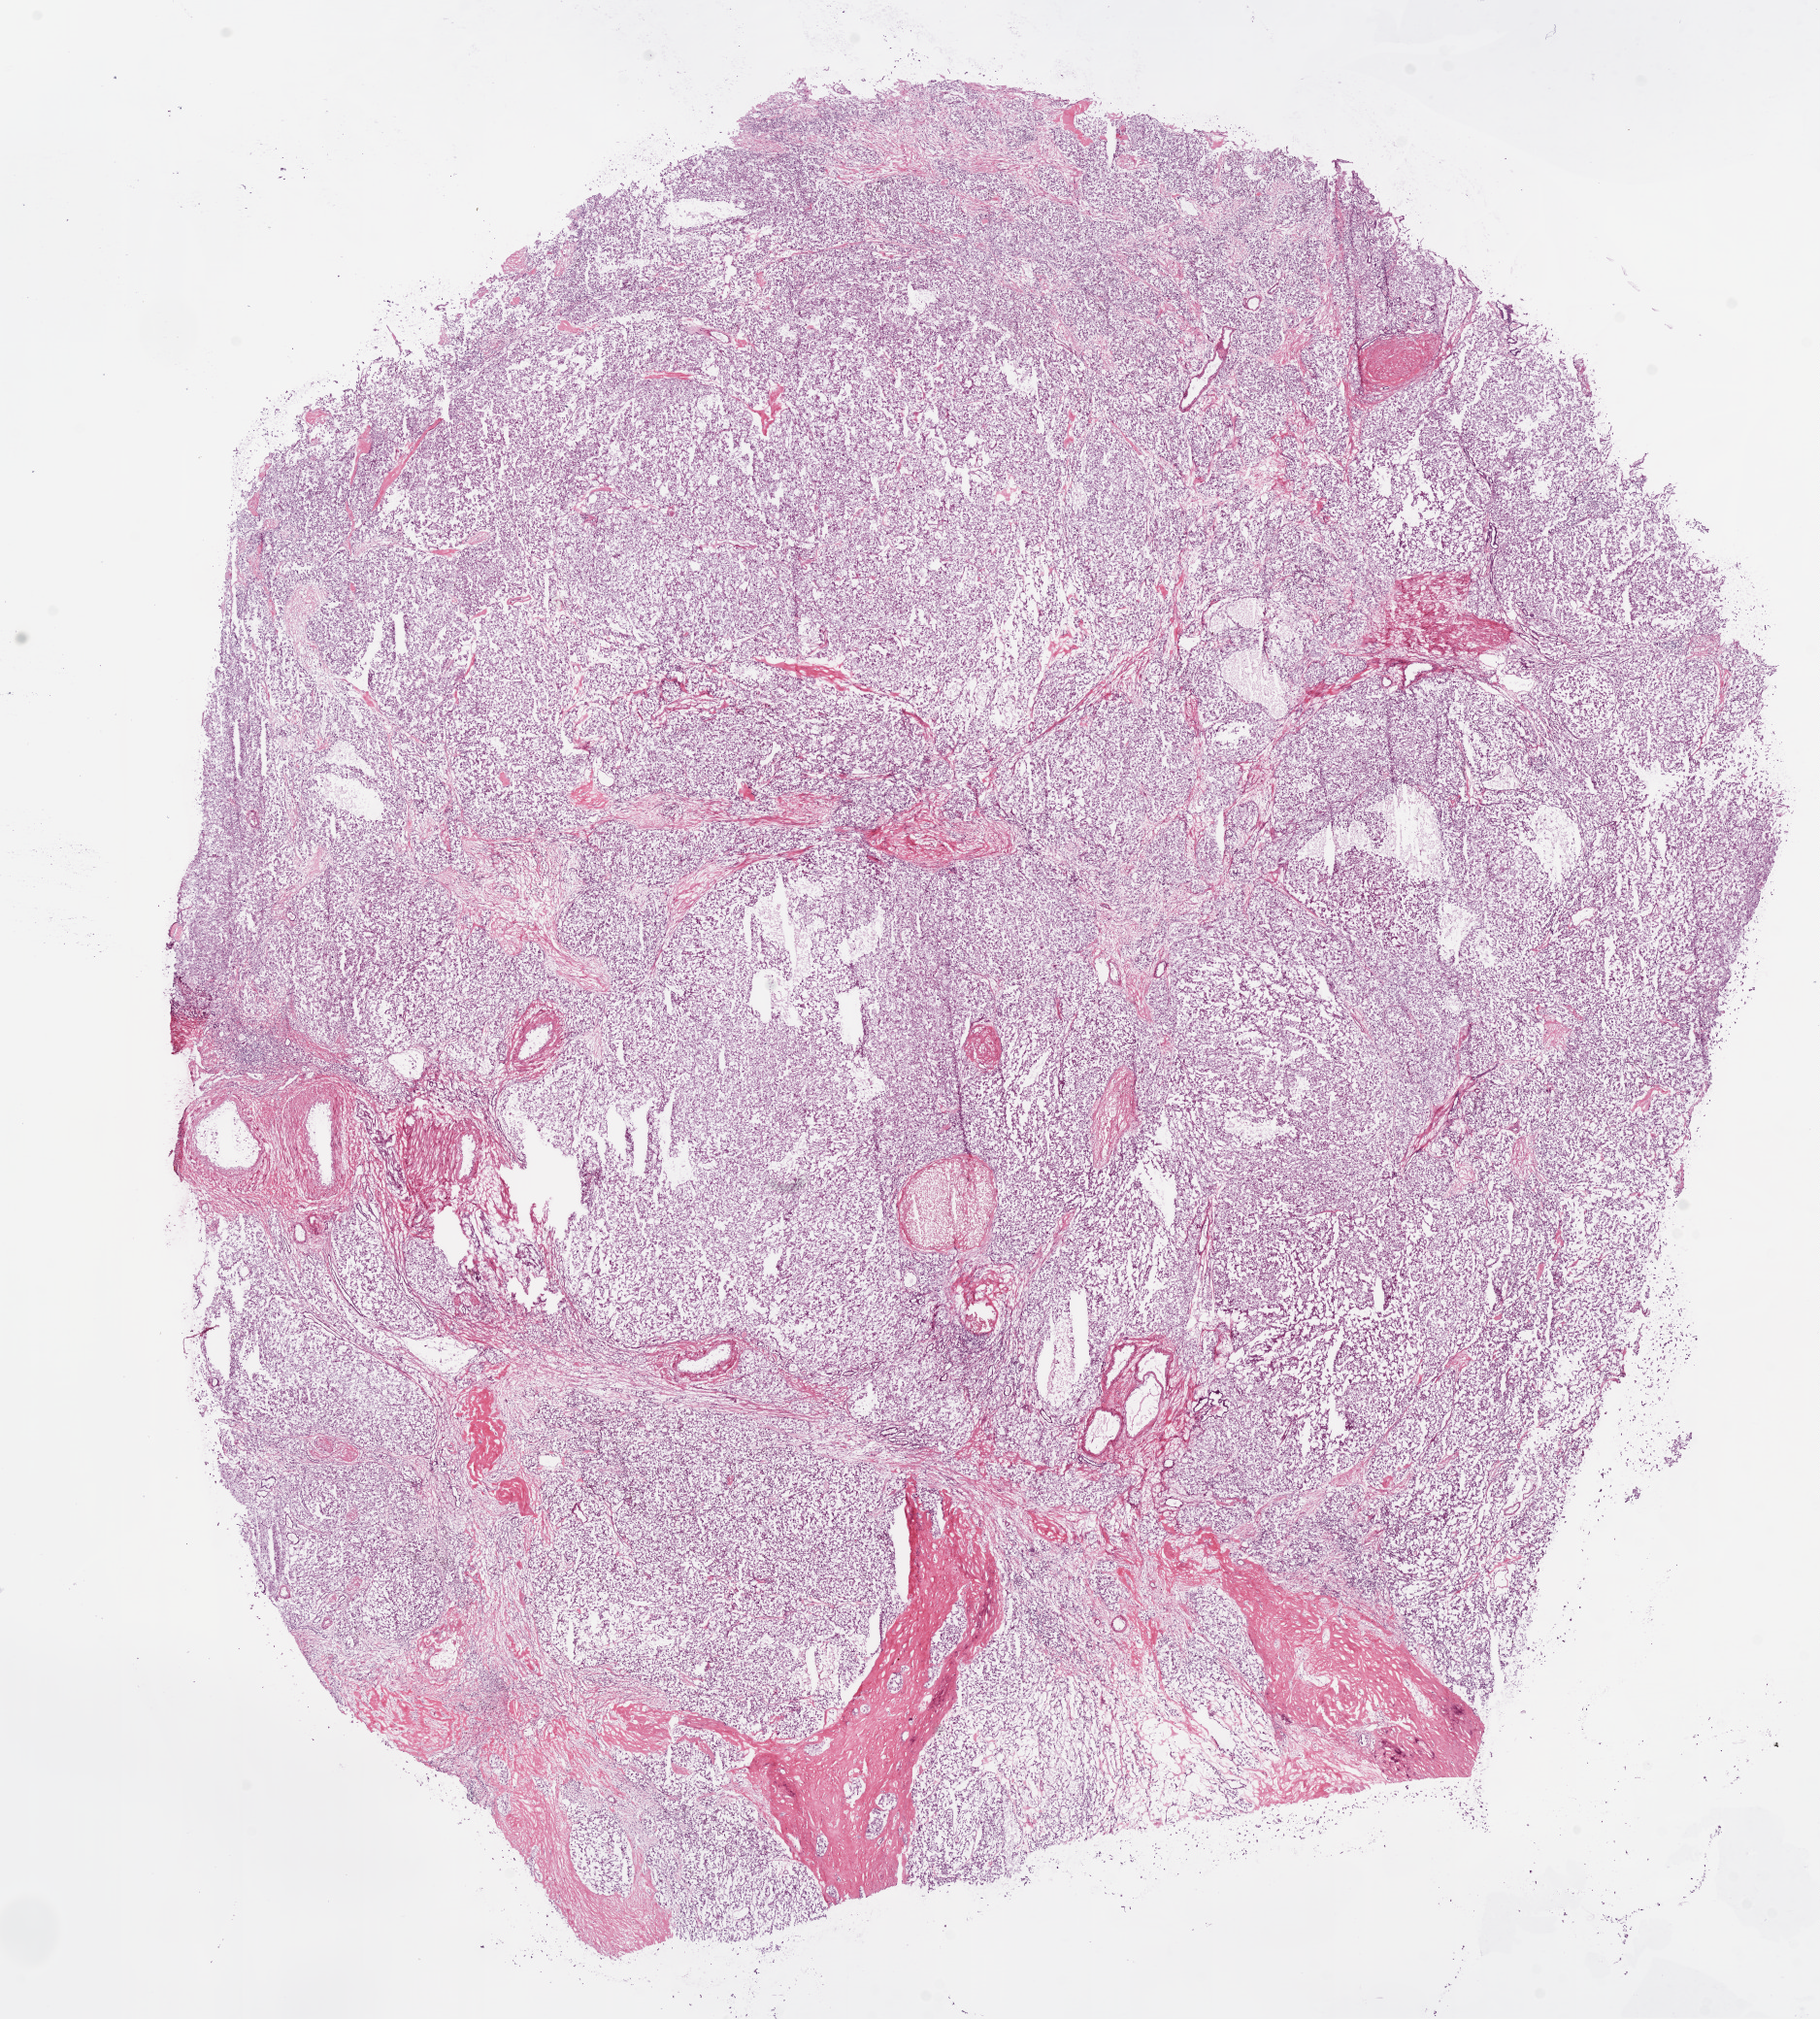
H&E-stained whole-slide image, low-resolution overview of the scanned area, about 15.0 x 16.7 mm (from a 20x scan). Frozen section from the bottom of the tissue portion. Sample: primary tumour, kidney. Male patient; age at initial diagnosis 63 years. Histologic grade: G3 (poorly differentiated). Slide review estimates, as recorded: tumour cells 82%, tumour nuclei 80%, normal cells 0%, stromal cells 15%, necrosis 3%.
• AJCC pathologic stage: I
• laterality: left
• diagnosis: Clear cell adenocarcinoma, NOS